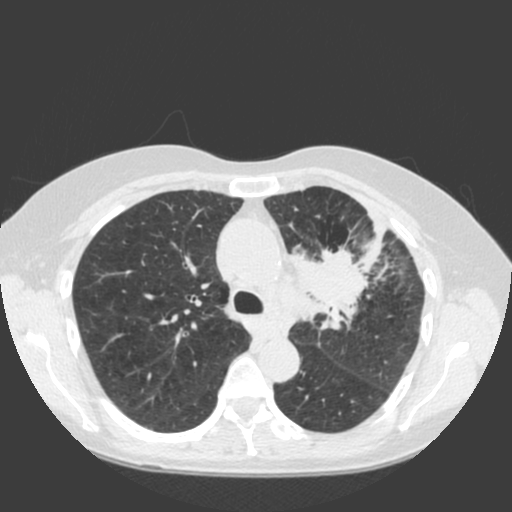
Axial slice from a low-dose chest CT screening exam. Baseline screening round. Lung window (W 1500 / L -600 HU). 2 mm slice thickness. Slice 54 of 184 in the series. 512 × 512 image matrix. Female participant, aged 66 years at enrolment. Current smoker at enrolment.
- Lesion marked by an expert reader, box from (x=283, y=231) to (x=398, y=334) px.
- The exam's reader record, not a measurement of the box and not confirmed to be the same lesion: non-calcified nodule or mass ≥4 mm, left upper lobe, 61 × 45 mm, spiculated (stellate) margins, soft tissue attenuation.
- Official screen result: positive, change unspecified: nodule(s) >= 4 mm or enlarging nodule(s), mass(es), or other non-specific abnormalities suspicious for lung cancer.
- Participant outcome: lung cancer diagnosed 19 days after this screen — squamous cell carcinoma, keratinizing, NOS, left upper lobe, left hilum, mediastinum, left main stem bronchus, other location, poorly differentiated (G3), stage IIIB (AJCC 6th edition), 60 mm at pathology.